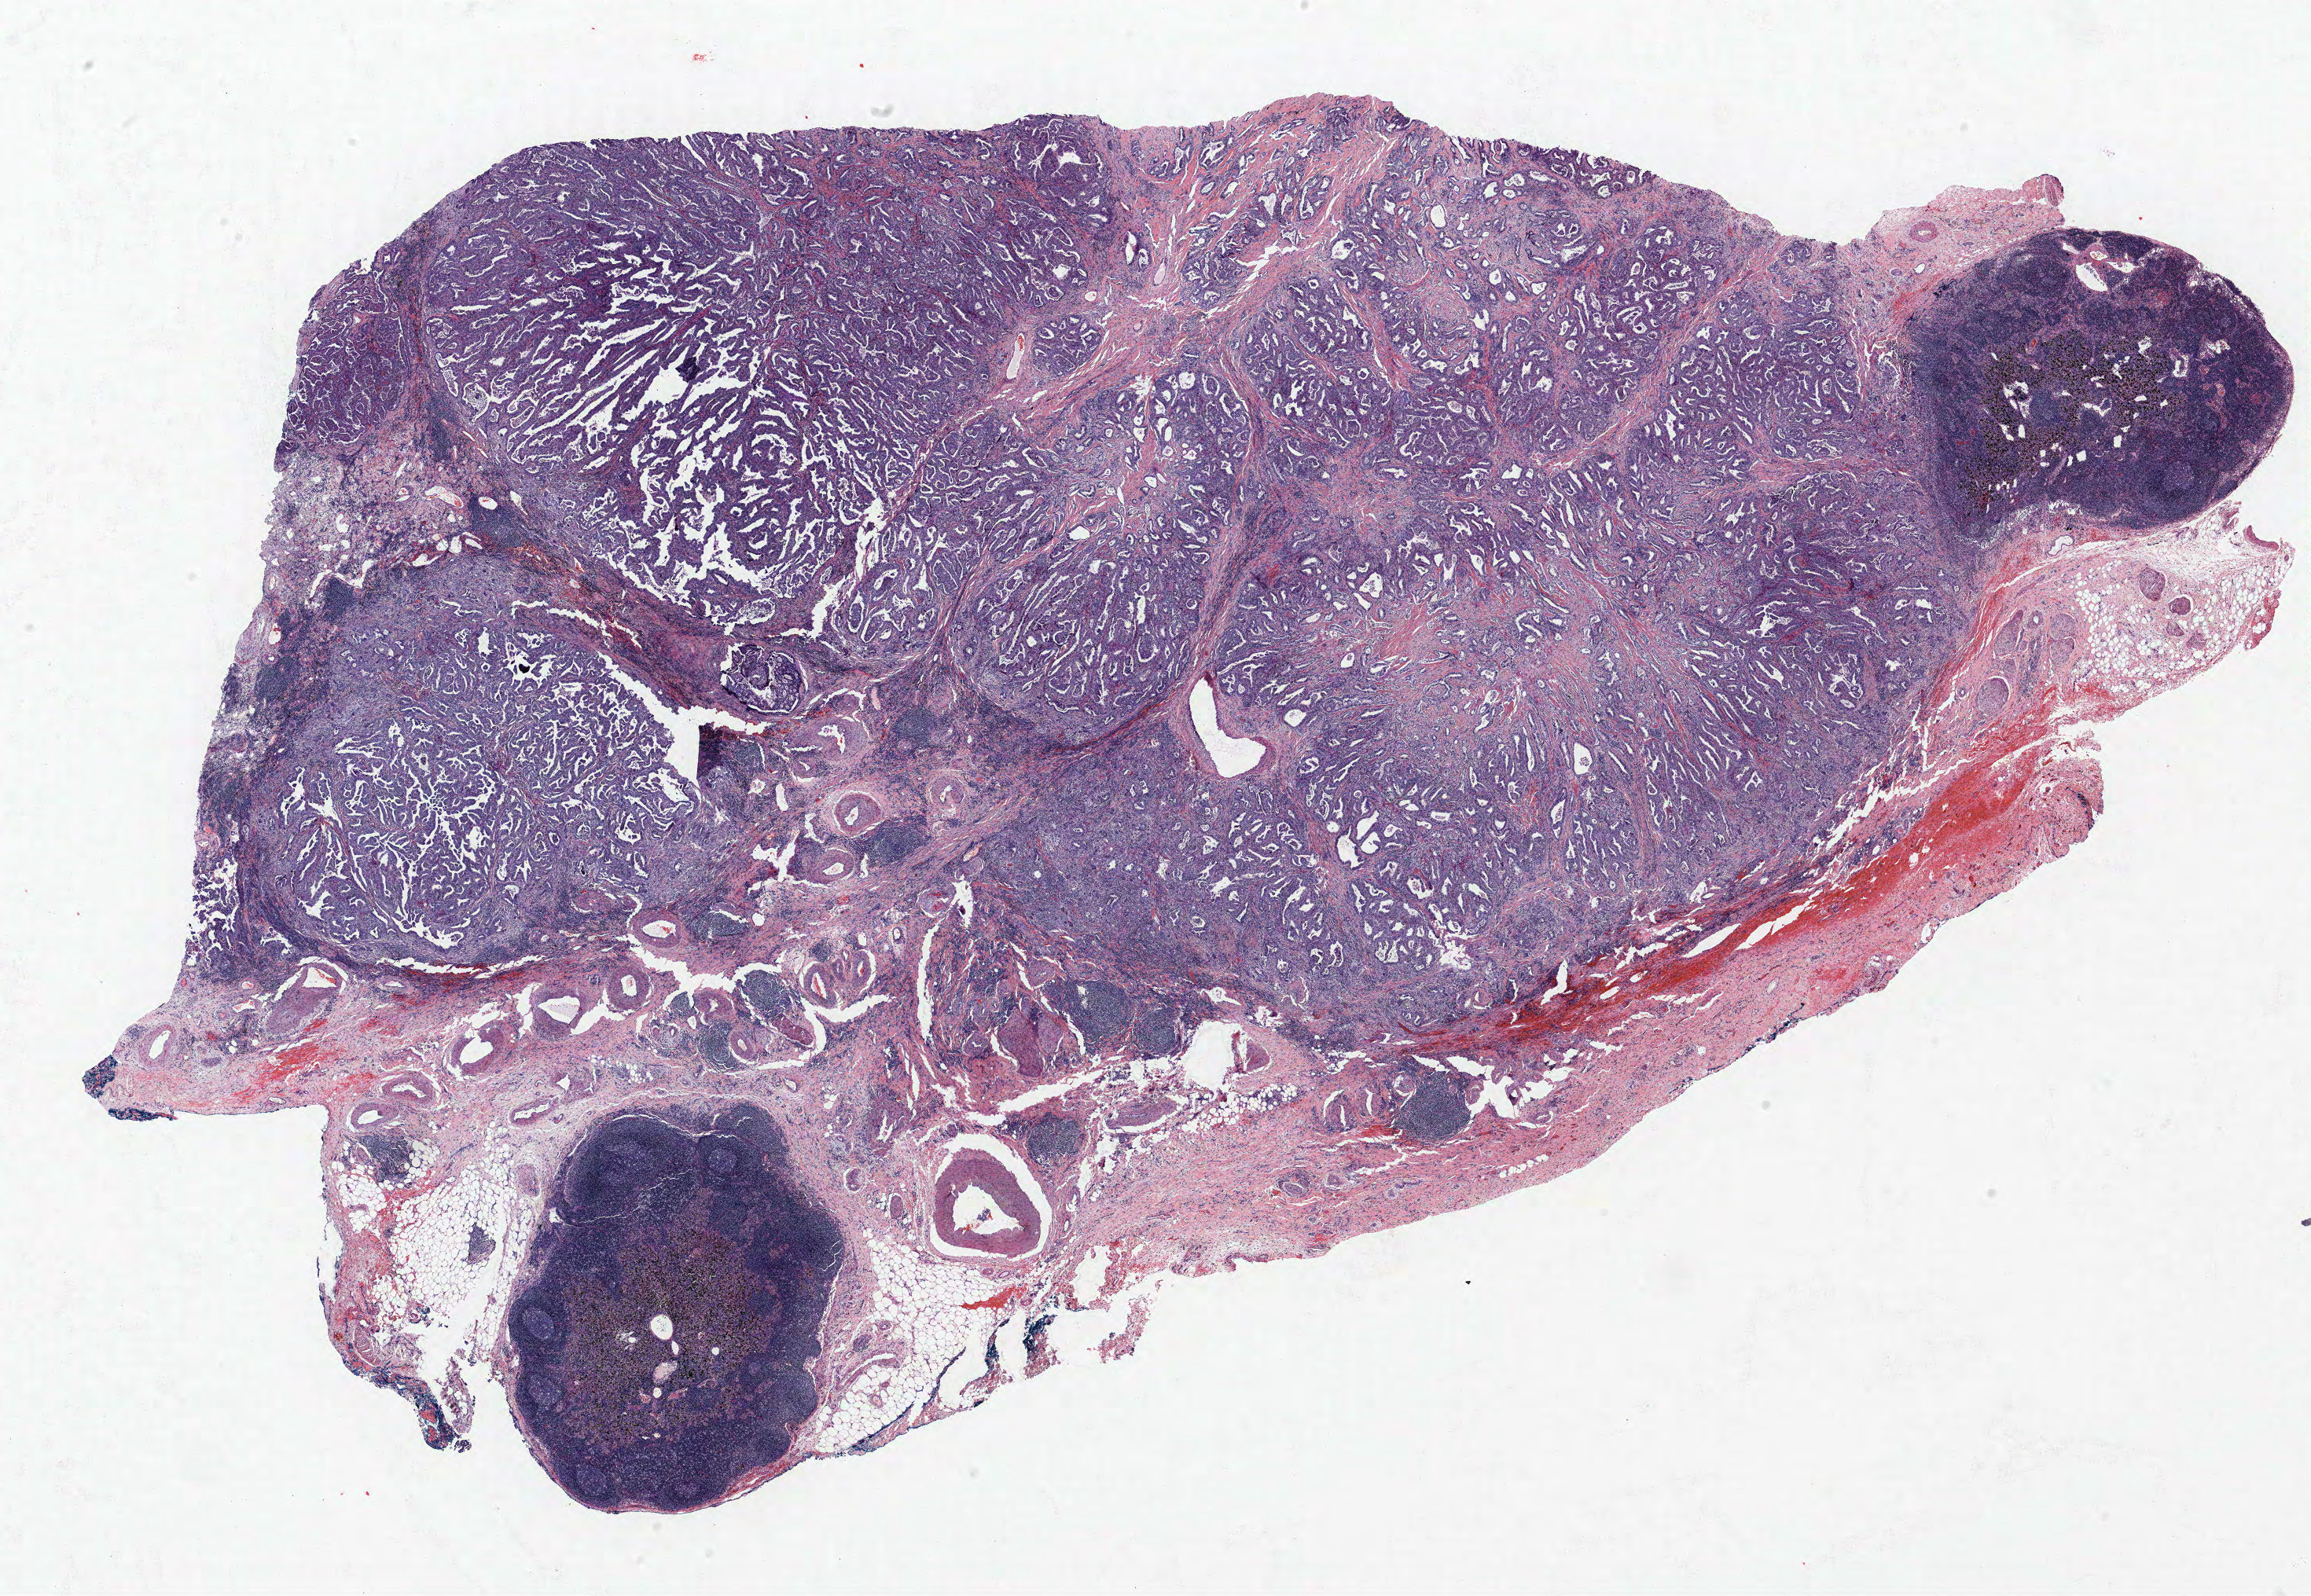
Whole-slide histology image, Hematoxylin and eosin (H&E) stained — whole scanned area (about 23.5 x 16.3 mm, slide scanned at 40x) shown as a low-resolution overview, FFPE section, lung tissue. Female patient, aged 68 at enrolment. Former smoker at enrolment.
Participant's lung-cancer diagnosis: Adenocarcinoma, NOS.